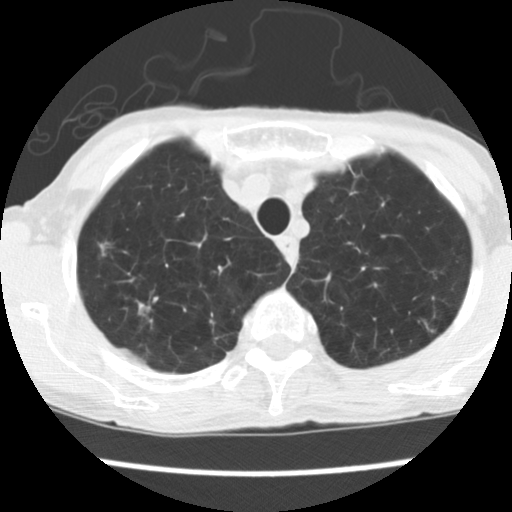
Axial slice from a low-dose chest CT screening exam. Baseline screening round. Lung window (W 1500 / L -600 HU). 2.5 mm slice thickness. Slice 25 of 160 in the series. 512 × 512 image matrix. Female, age 70 years at enrolment. Former smoker at enrolment.
2 expert-annotated lung lesions on this slice (largest first), bounding box [x1, y1, x2, y2] px = [118, 285, 179, 342]; [77, 223, 132, 275]. Screening reader's record for this exam: no non-calcified nodule ≥4 mm recorded. Official screen result: negative screen, significant abnormalities not suspicious for lung cancer.